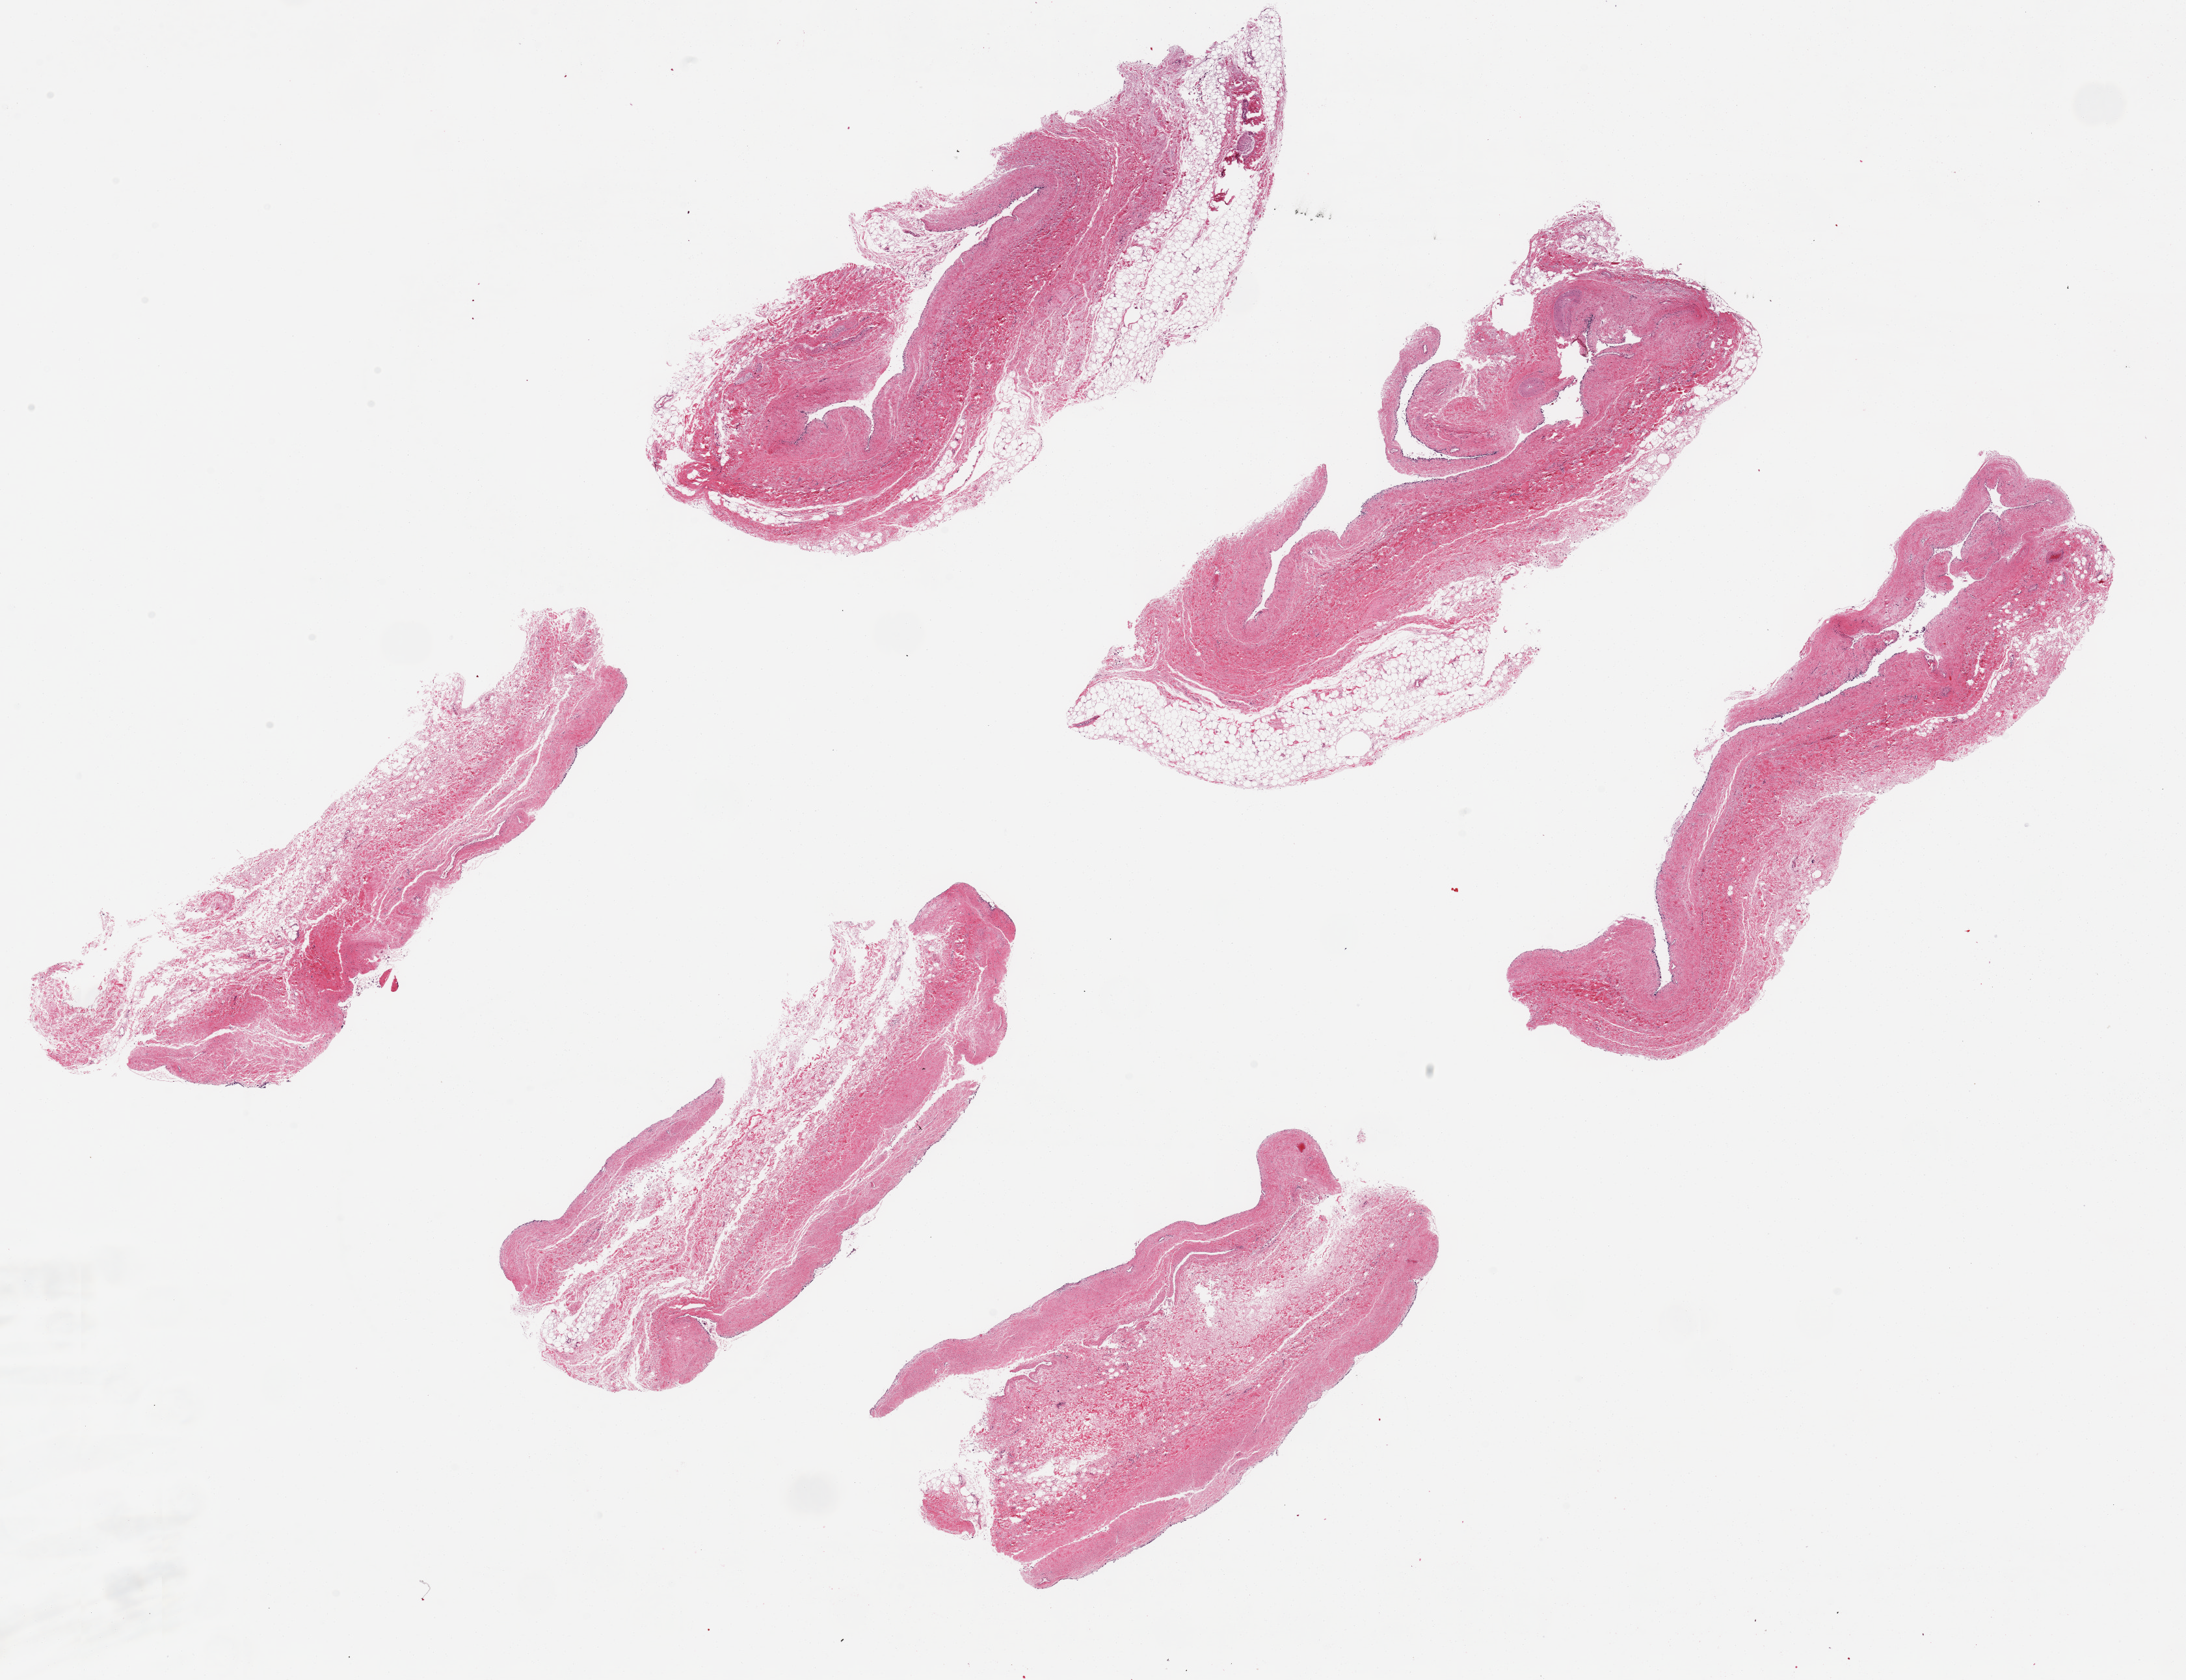
H&E whole-slide image — low-resolution overview of the scanned area, about 26.6 x 20.4 mm. PAXgene-fixed paraffin-embedded (PFPE) section. Sampled site (target tissue): urinary bladder. Donor tissue sample. Donor: male.
• review note (as recorded): 6 ~9x2.5mm pieces; Urothelium completely sloughed; a few minute foci badly autolyzed